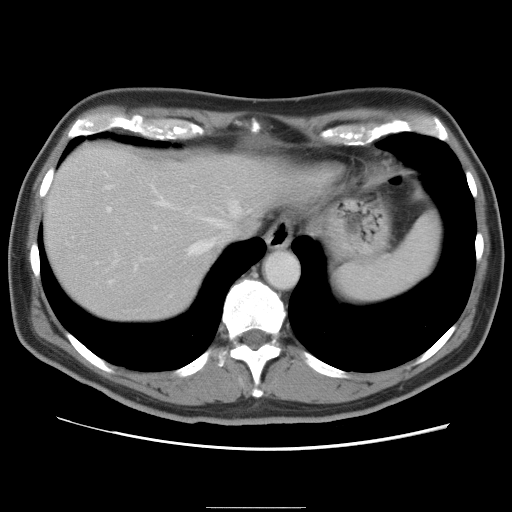
Contrast-enhanced abdominal CT, one axial slice; slice 69 of 87 in the series (ordered by position); 120 kVp; intravenous contrast given; soft-tissue window (W 400 / L 40 HU); 5 mm slice thickness; 512 × 512 image matrix. Male patient, age 63 years. From the clinical record (not read from this slice): diagnosis: colorectal cancer liver metastases, imaged before liver resection; multiple liver metastases: no; largest metastasis: 9 cm; chemotherapy before resection: no.
Annotated regions visible in this slice (manually delineated by an expert):
- hepatic veins: bounding box (x1, y1, x2, y2) in pixels: (96, 184, 242, 264)
- liver: (44, 146, 294, 322)
- planned liver remnant (the part of the liver to remain after resection): (44, 166, 216, 321)
- portal vein (with intrahepatic branches): (105, 206, 159, 285)